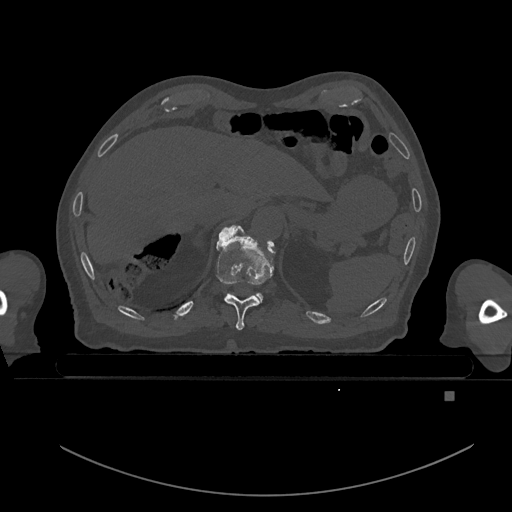
CT including the spine, one axial slice. Position 74 of 969 along the scan axis. Bone window (W 1800 / L 400 HU). 0.5 mm slice thickness. 512 × 512 image matrix, field of view 456 × 456 mm. Male patient, age 82 years. Case-level facts recorded for this patient, not image findings: primary cancer: prostate; vertebrae with lytic lesions (as recorded): T11, T9, T8, T2.
Structures marked on this image (semi-automatically segmented with operator editing):
- T10 vertebra: bounding box <216,225,274,331> (left, top, right, bottom; pixels)
- T11 vertebra: <228,293,263,302>